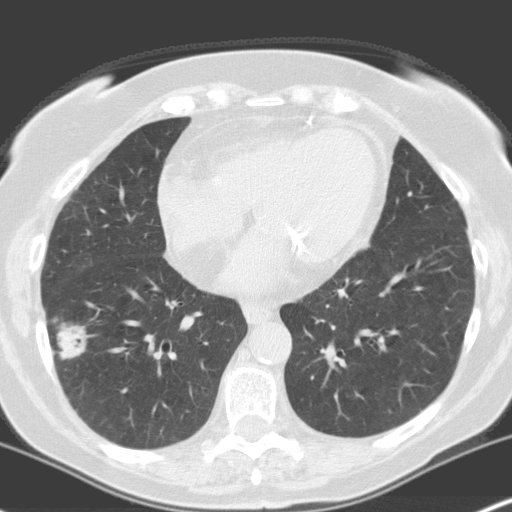
Low-dose screening chest CT, one axial slice. Position 71 of 160 along the scan axis. Lung window (W 1500 / L -600 HU). 3.2 mm slice thickness. 512 × 512 image matrix, field of view 316 × 316 mm.
Outlined on this slice (expert manual segmentation):
- lesion 1 (tumor, lower lobe of right lung): bounding box (x1, y1, x2, y2) in pixels: (57, 324, 87, 360)